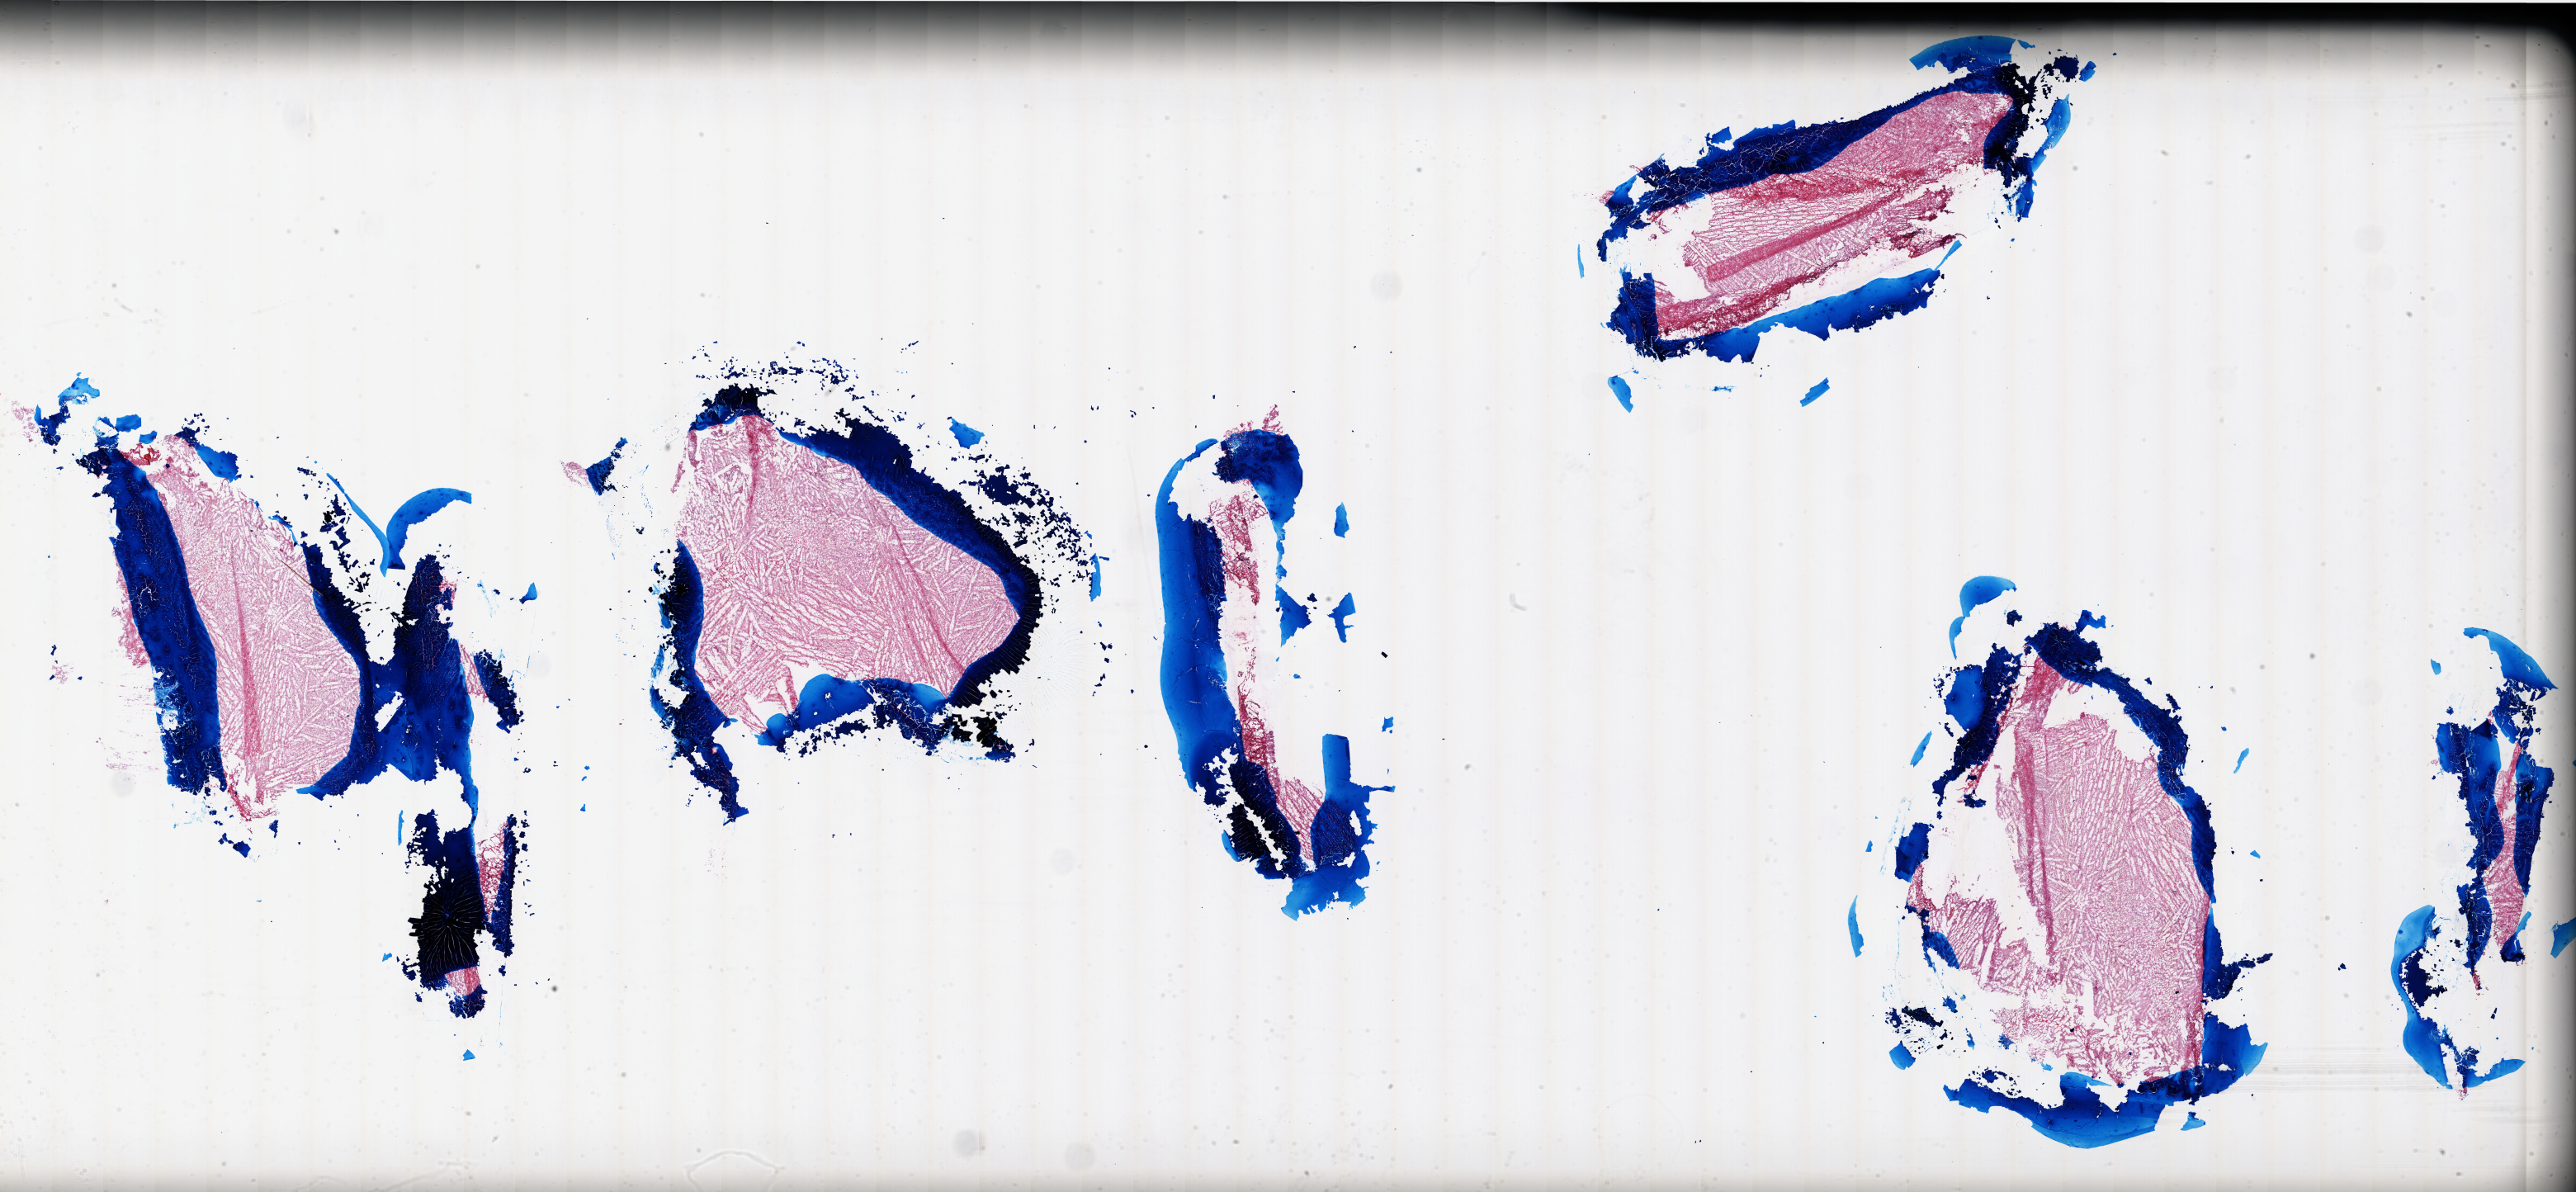
Whole-slide histology image, H&E, whole scanned area (about 49.9 x 23.1 mm) shown as a low-resolution overview; frozen section from the top of the tissue portion; brain, primary tumour sample. Patient: male, age at initial diagnosis 60 years. Pathologist review of this section (percent, as recorded): tumour cells 90%, tumour nuclei 100%, normal cells 0%, stromal cells 0%, necrosis 10%.
Pathologic diagnosis: Glioblastoma.